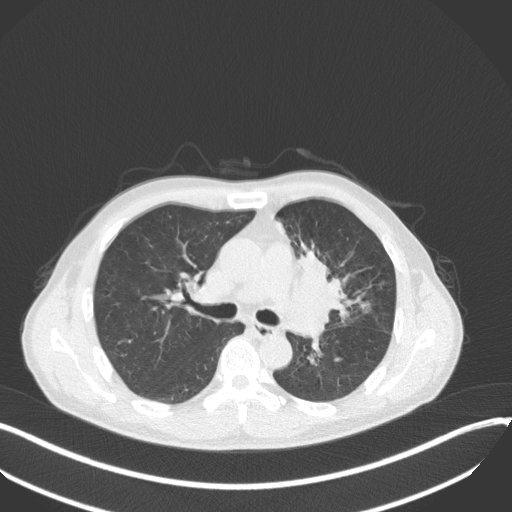
Chest CT, one axial slice; slice 206 of 411 in the series (ordered by position); reconstruction kernel B31f; lung window (W 1500 / L -600 HU); 1 mm slice thickness; 512 × 512 image matrix, field of view 400 × 400 mm. Male patient, age 56 years. Case-level facts recorded for this patient, not image findings: clinical TNM (as recorded): T2a N0 M0.
Structures marked on this image (rectangle marked by the reading radiologist):
- lung tumour (recorded histology: squamous cell carcinoma): bounding box <284,241,353,327> (left, top, right, bottom; pixels)